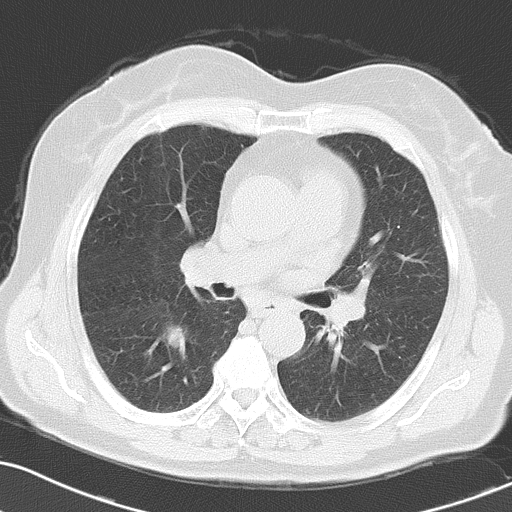
Chest CT, one axial slice; reconstruction kernel B70f; 120 kVp; lung window (W 1500 / L -600 HU); 5 mm slice thickness; 512 × 512 image matrix, field of view 323 × 323 mm. Patient: female, 70 years. From the clinical record (not read from this slice): clinical TNM (as recorded): T1c N3 M0.
Outlined on this slice (rectangle marked by the reading radiologist):
- lung tumour (recorded histology: small cell carcinoma): box from (x=152, y=315) to (x=189, y=350) px